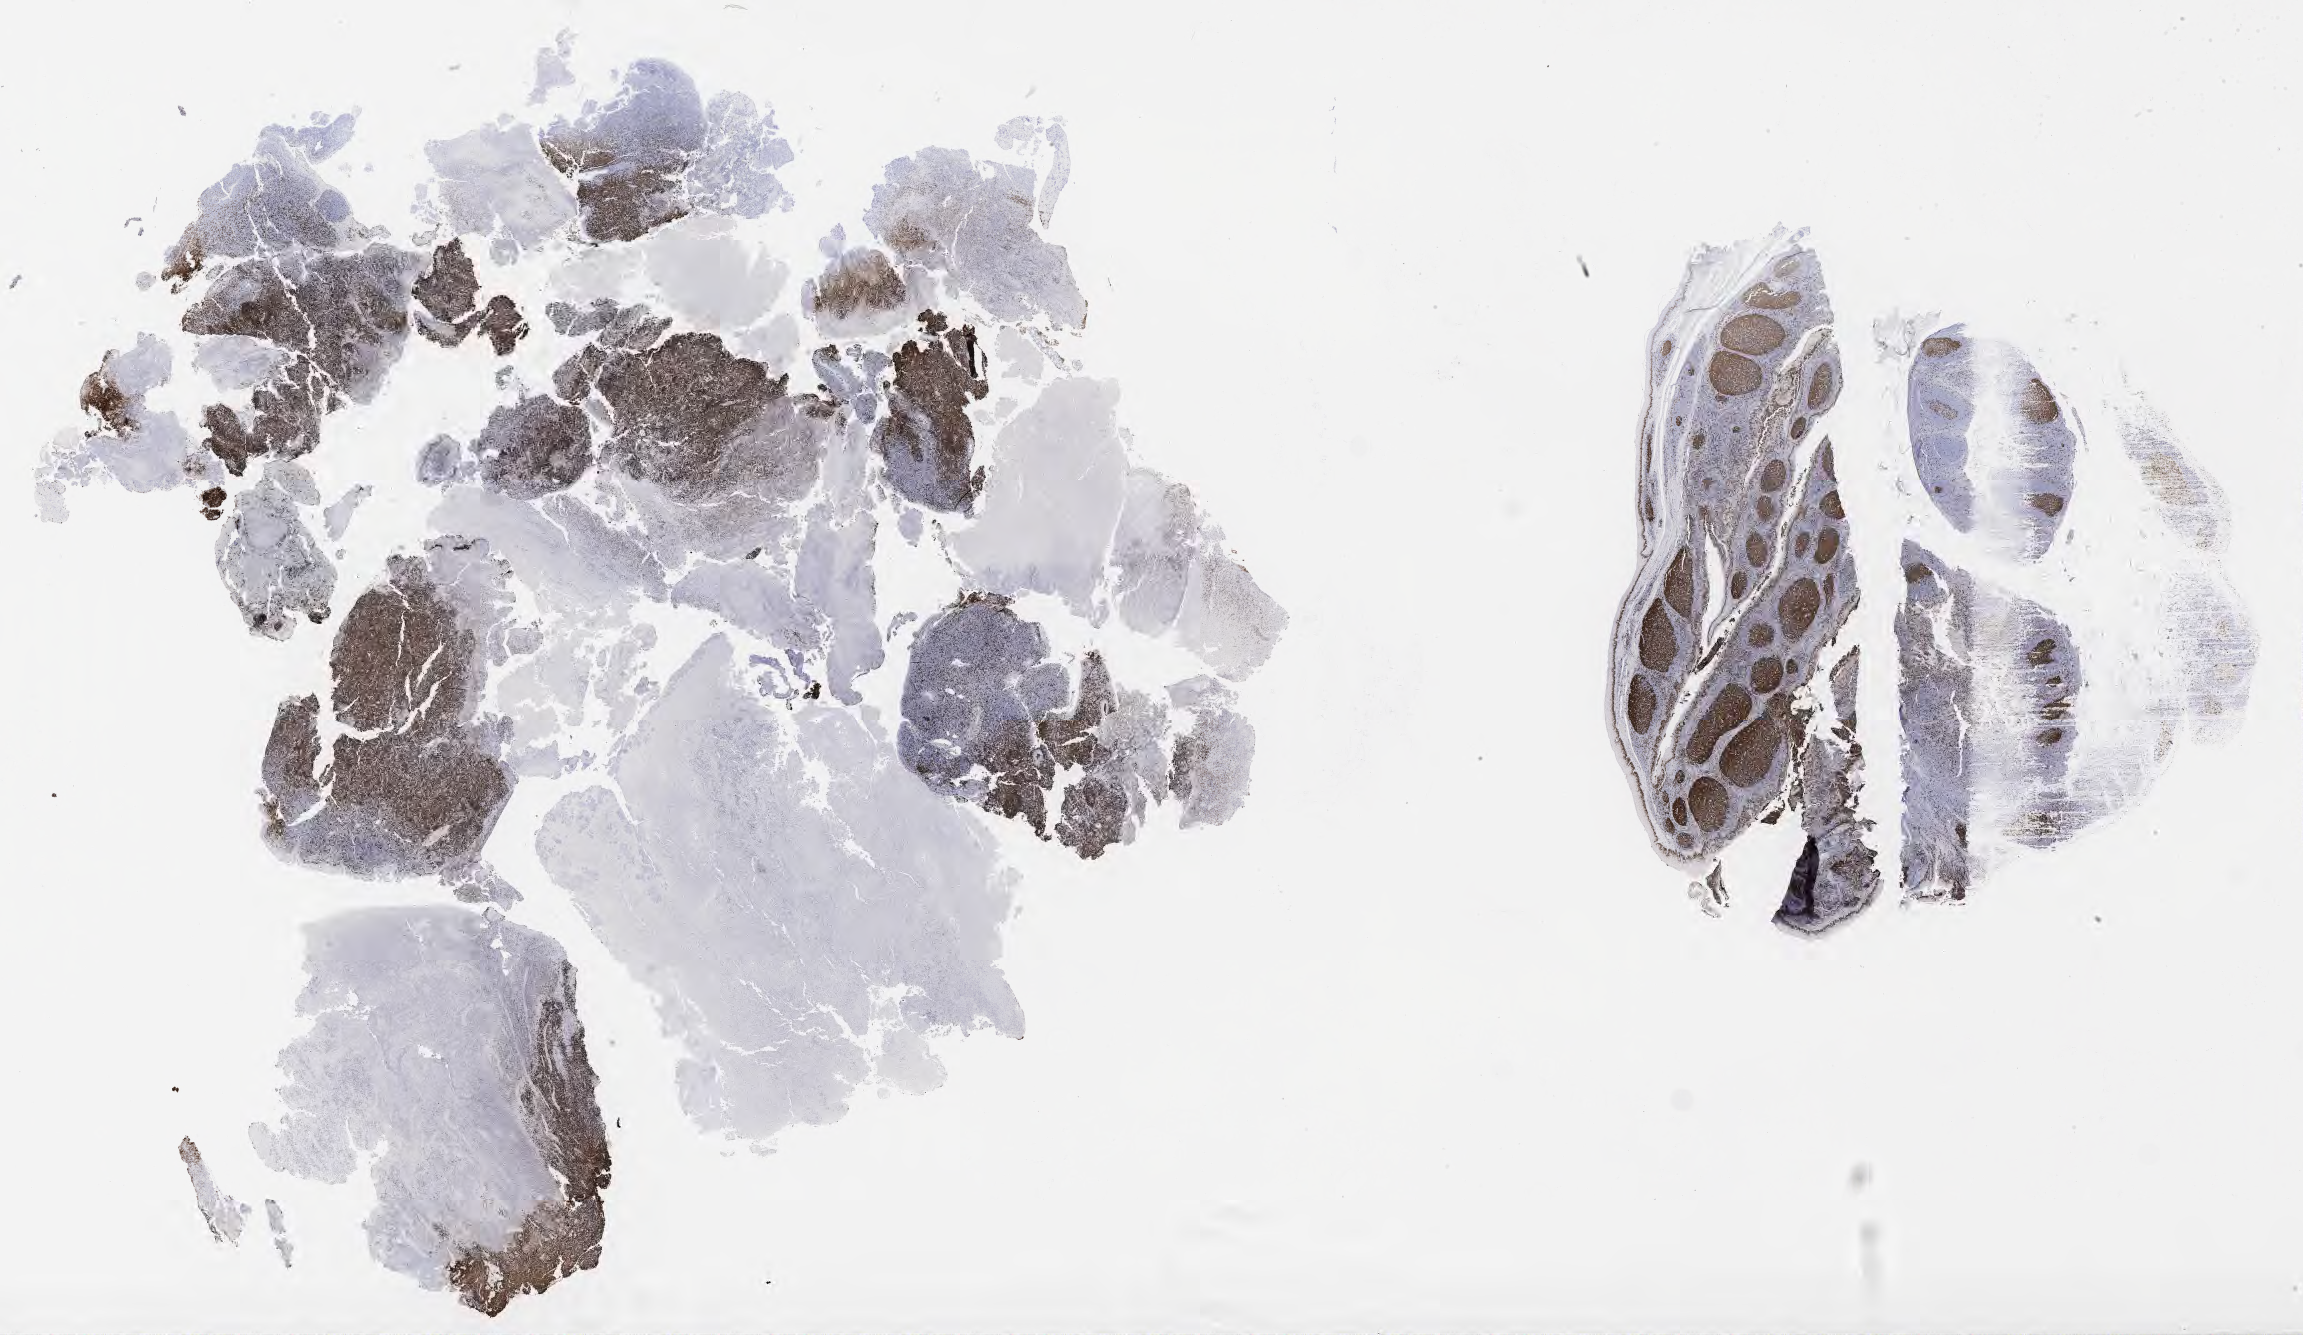
IHC for Ki-67, whole-slide image, shown as a low-resolution overview of the whole scanned area (about 37.2 x 21.6 mm); specimen: tumor tissue. Patient male; aged 47.
• histologic diagnosis: Diffuse large B-cell lymphoma, NOS